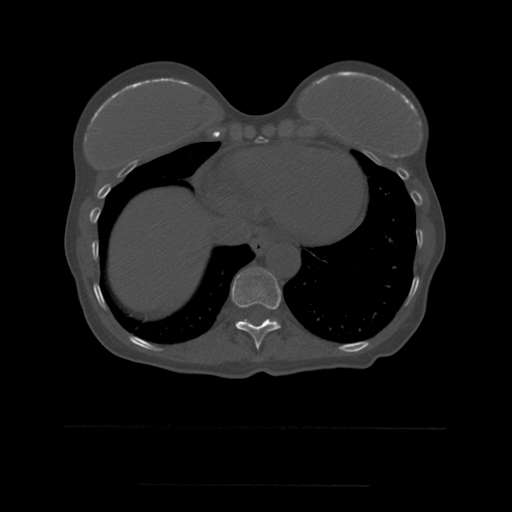
CT including the spine, one axial slice. Slice 298 of 544 in the series (ordered by position). Bone window (W 1800 / L 400 HU). 1.25 mm slice thickness. 512 × 512 image matrix. Patient age 58 years. Case-level facts recorded for this patient, not image findings: primary cancer: lung.
Annotated regions visible in this slice (semi-automatic segmentation, software-assisted and operator-edited):
- T10 vertebra: bounding box (x1, y1, x2, y2) in pixels: (232, 268, 281, 349)
- T11 vertebra: (240, 320, 278, 322)